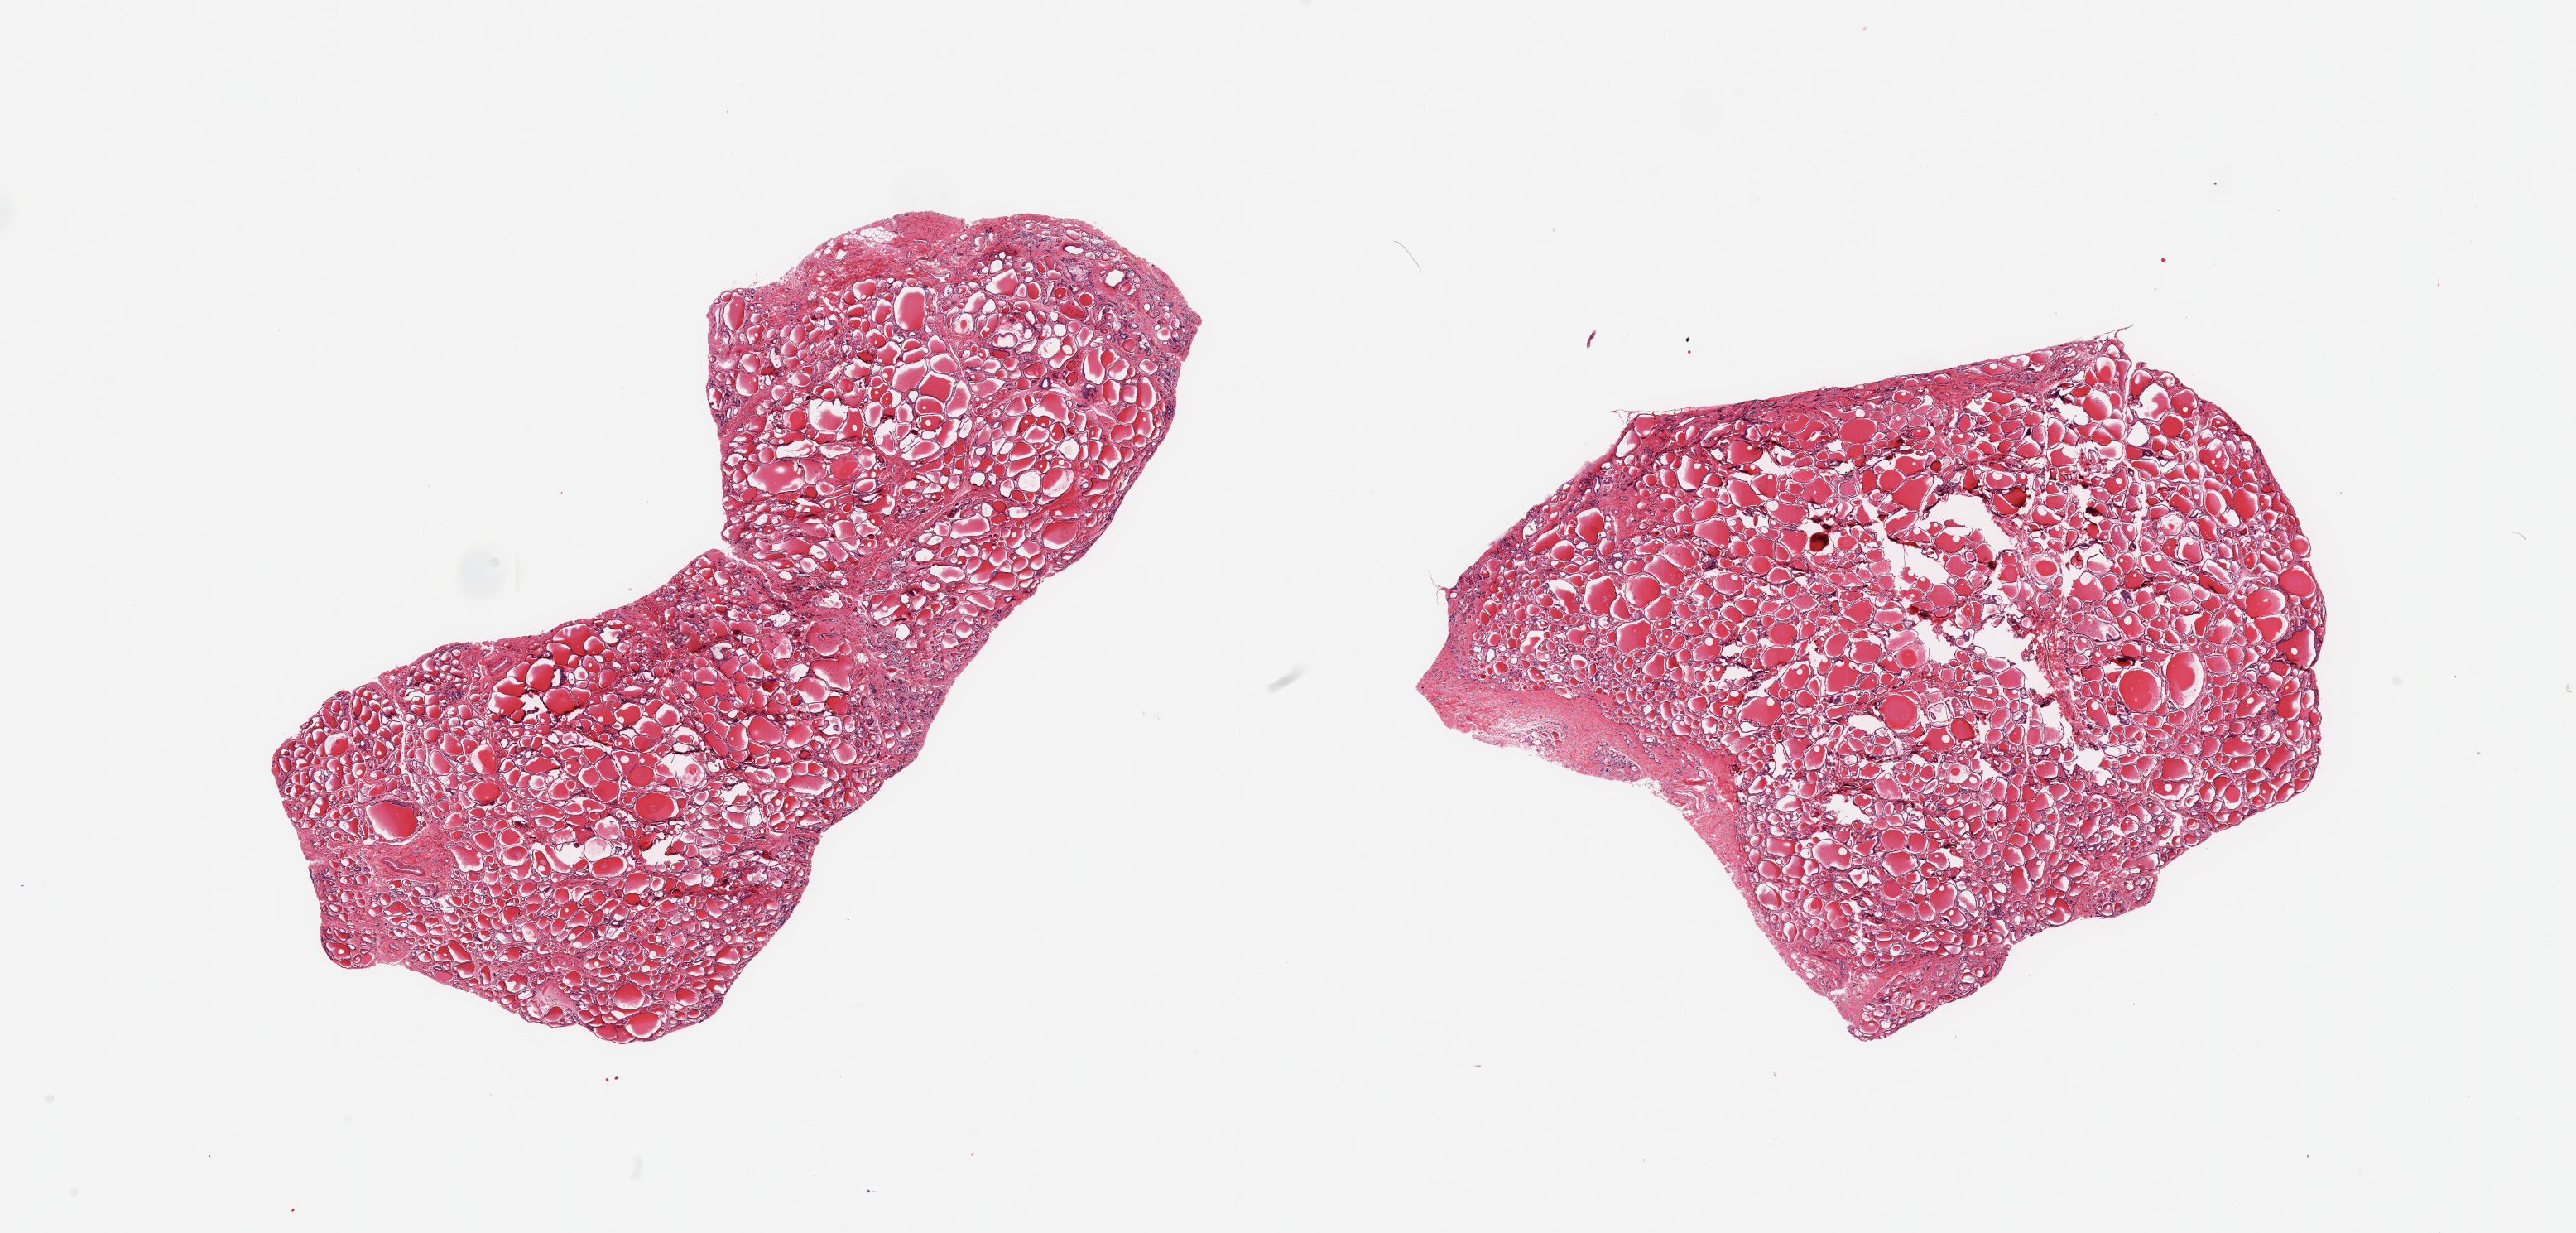
Hematoxylin and eosin (H&E) whole-slide image, brightfield, whole scanned area (about 24.6 x 11.8 mm) shown as a low-resolution overview, PAXgene-fixed, paraffin-embedded tissue, sampled site (target tissue): thyroid, tissue donor sample. Donor: female.
Pathologist's review note for this sample: 2 pieces, no abnormalities.